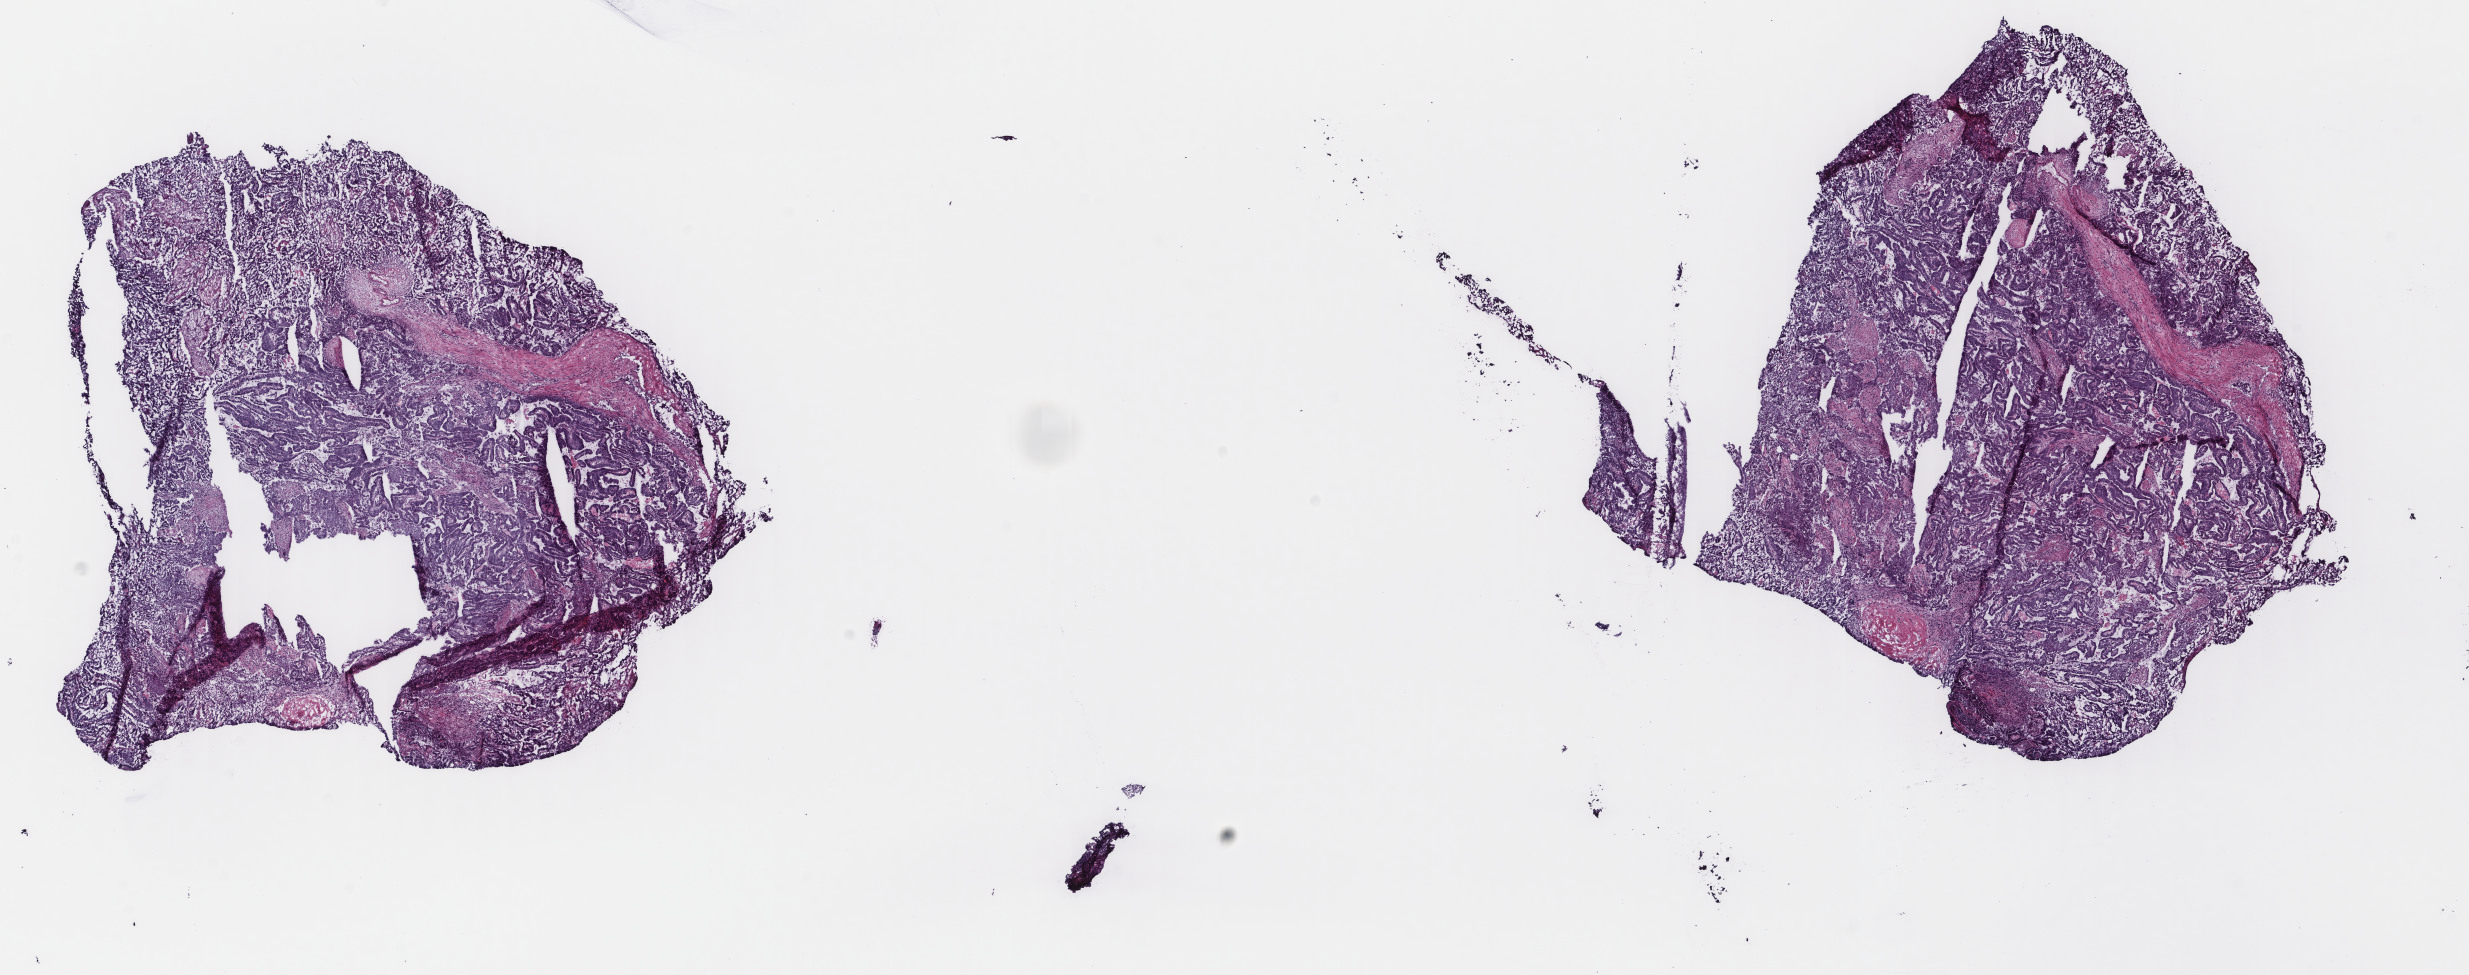
Digitized H&E-stained tissue section (whole slide) — whole scanned area (about 19.6 x 7.7 mm) shown as a low-resolution overview. Frozen section. Uterus, primary tumour sample. Female, age 54 years at initial diagnosis. Histologic grade: G1 (well differentiated). Slide review estimates, as recorded: tumour cells 80%, tumour nuclei 80%, normal cells 0%, stromal cells 10%, necrosis 10%. Inflammatory infiltration, as recorded: lymphocyte infiltration 40%, monocyte infiltration 20%, neutrophil infiltration 20%.
- FIGO stage: IA
- histologic diagnosis: Endometrioid adenocarcinoma, NOS (endometrium)